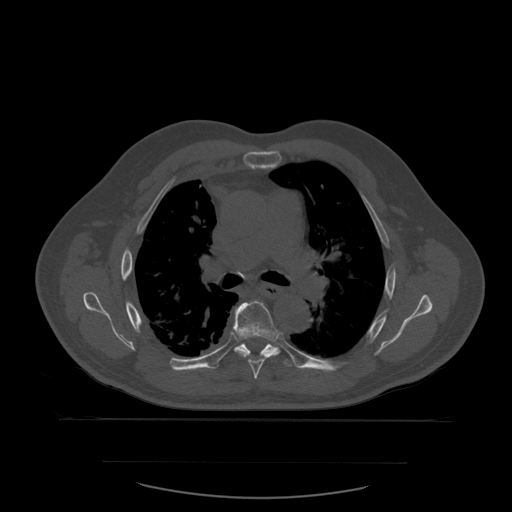
CT including the spine, one axial slice; slice 397 of 590 in the series (ordered by position); bone window (W 1800 / L 400 HU); 1.25 mm slice thickness; 512 × 512 image matrix, field of view 479 × 479 mm. Patient age 71 years. From the clinical record (not read from this slice): primary cancer: lung.
Annotated regions visible in this slice (semi-automatic segmentation, software-assisted and operator-edited):
- T6 vertebra: bounding box [x1, y1, x2, y2] px = [233, 301, 279, 380]
- T7 vertebra: [233, 308, 292, 367]